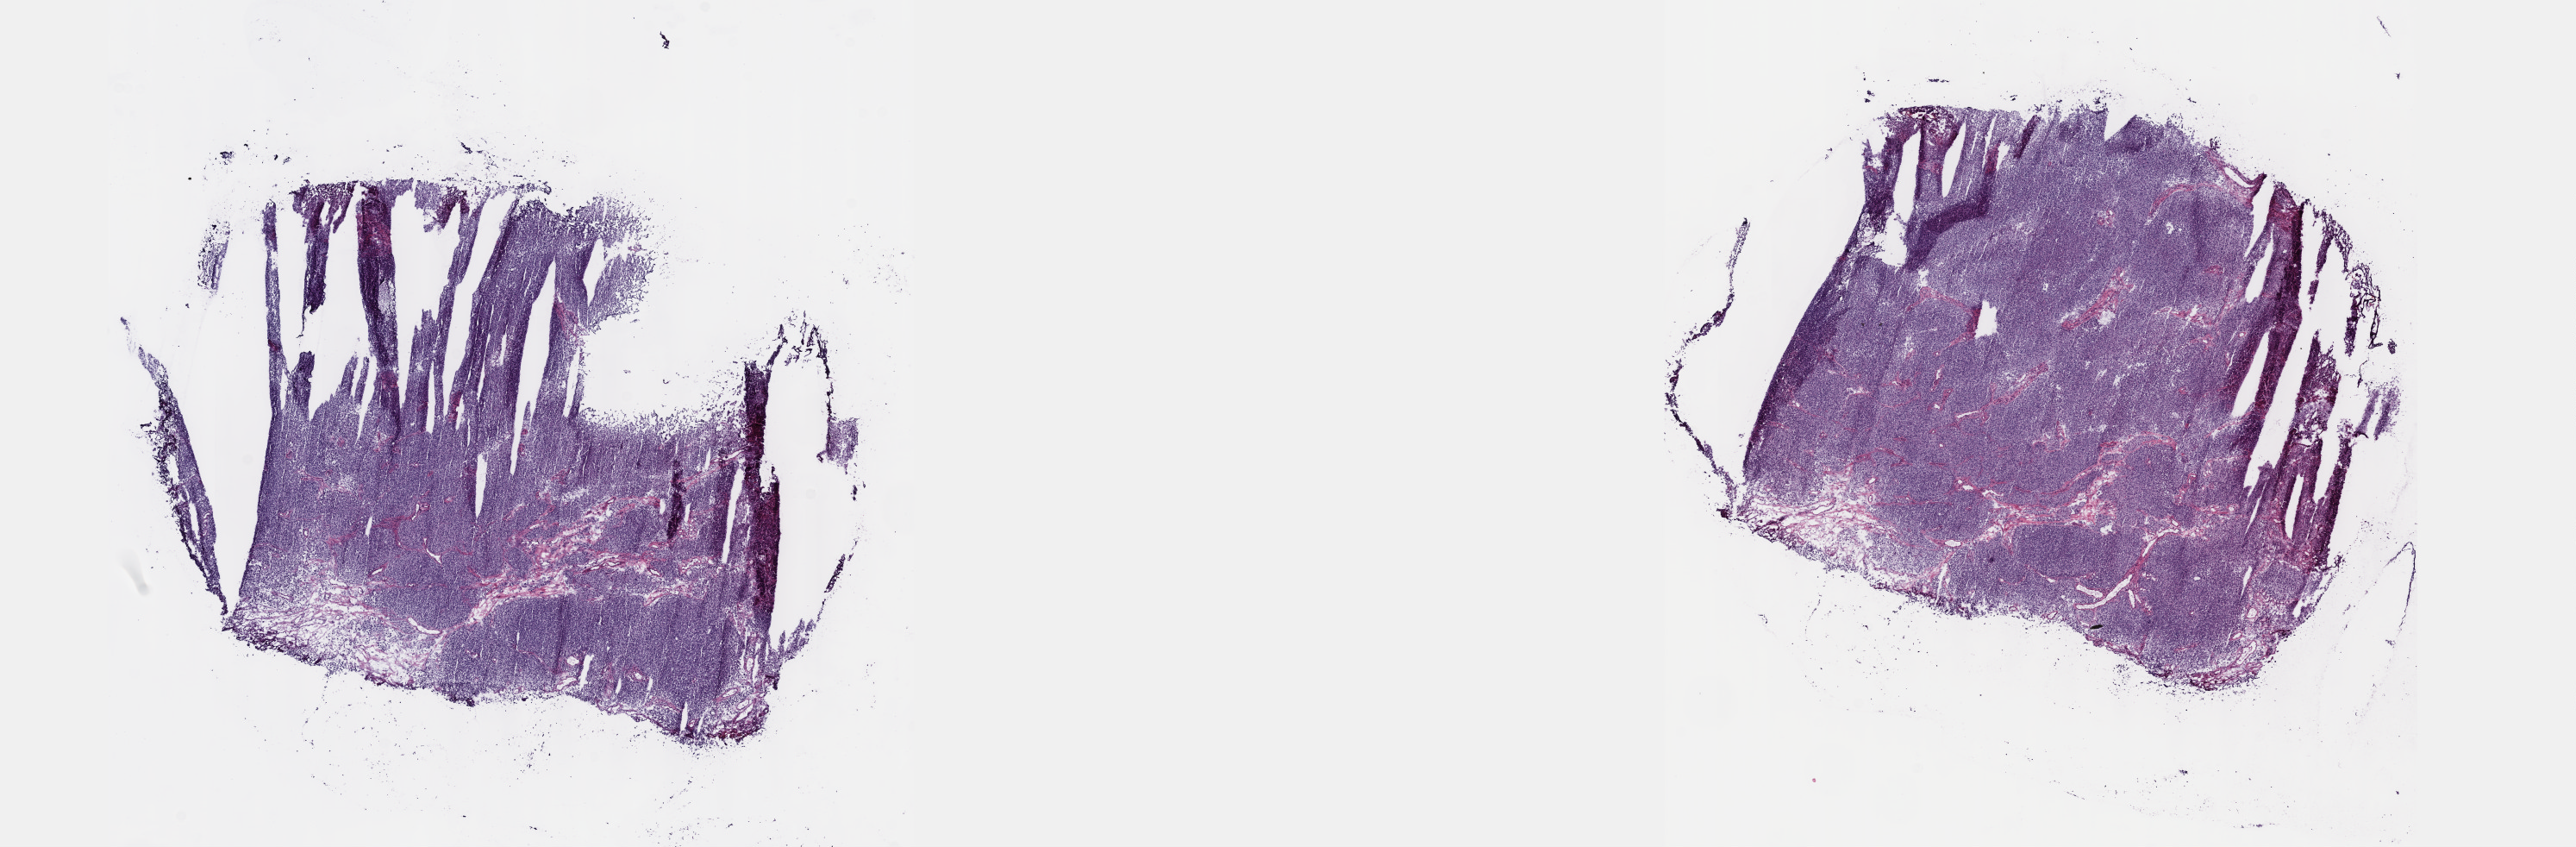
Digitized Hematoxylin and eosin (H&E) stained tissue section (whole slide) — shown as a low-resolution overview of the whole scanned area (about 24.1 x 7.9 mm), frozen section, prostate, primary tumour sample. Male, age 59 years at initial diagnosis. Gleason score: 10 (5+5). Composition of this section per pathologist review: tumour cells 90%, tumour nuclei 95%, normal cells 0%, stromal cells 10%, necrosis 0%. Inflammatory infiltration, as recorded: lymphocyte infiltration 0%, monocyte infiltration 0%, neutrophil infiltration 0%.
Histologic diagnosis: Adenocarcinoma, NOS. Laterality: bilateral.